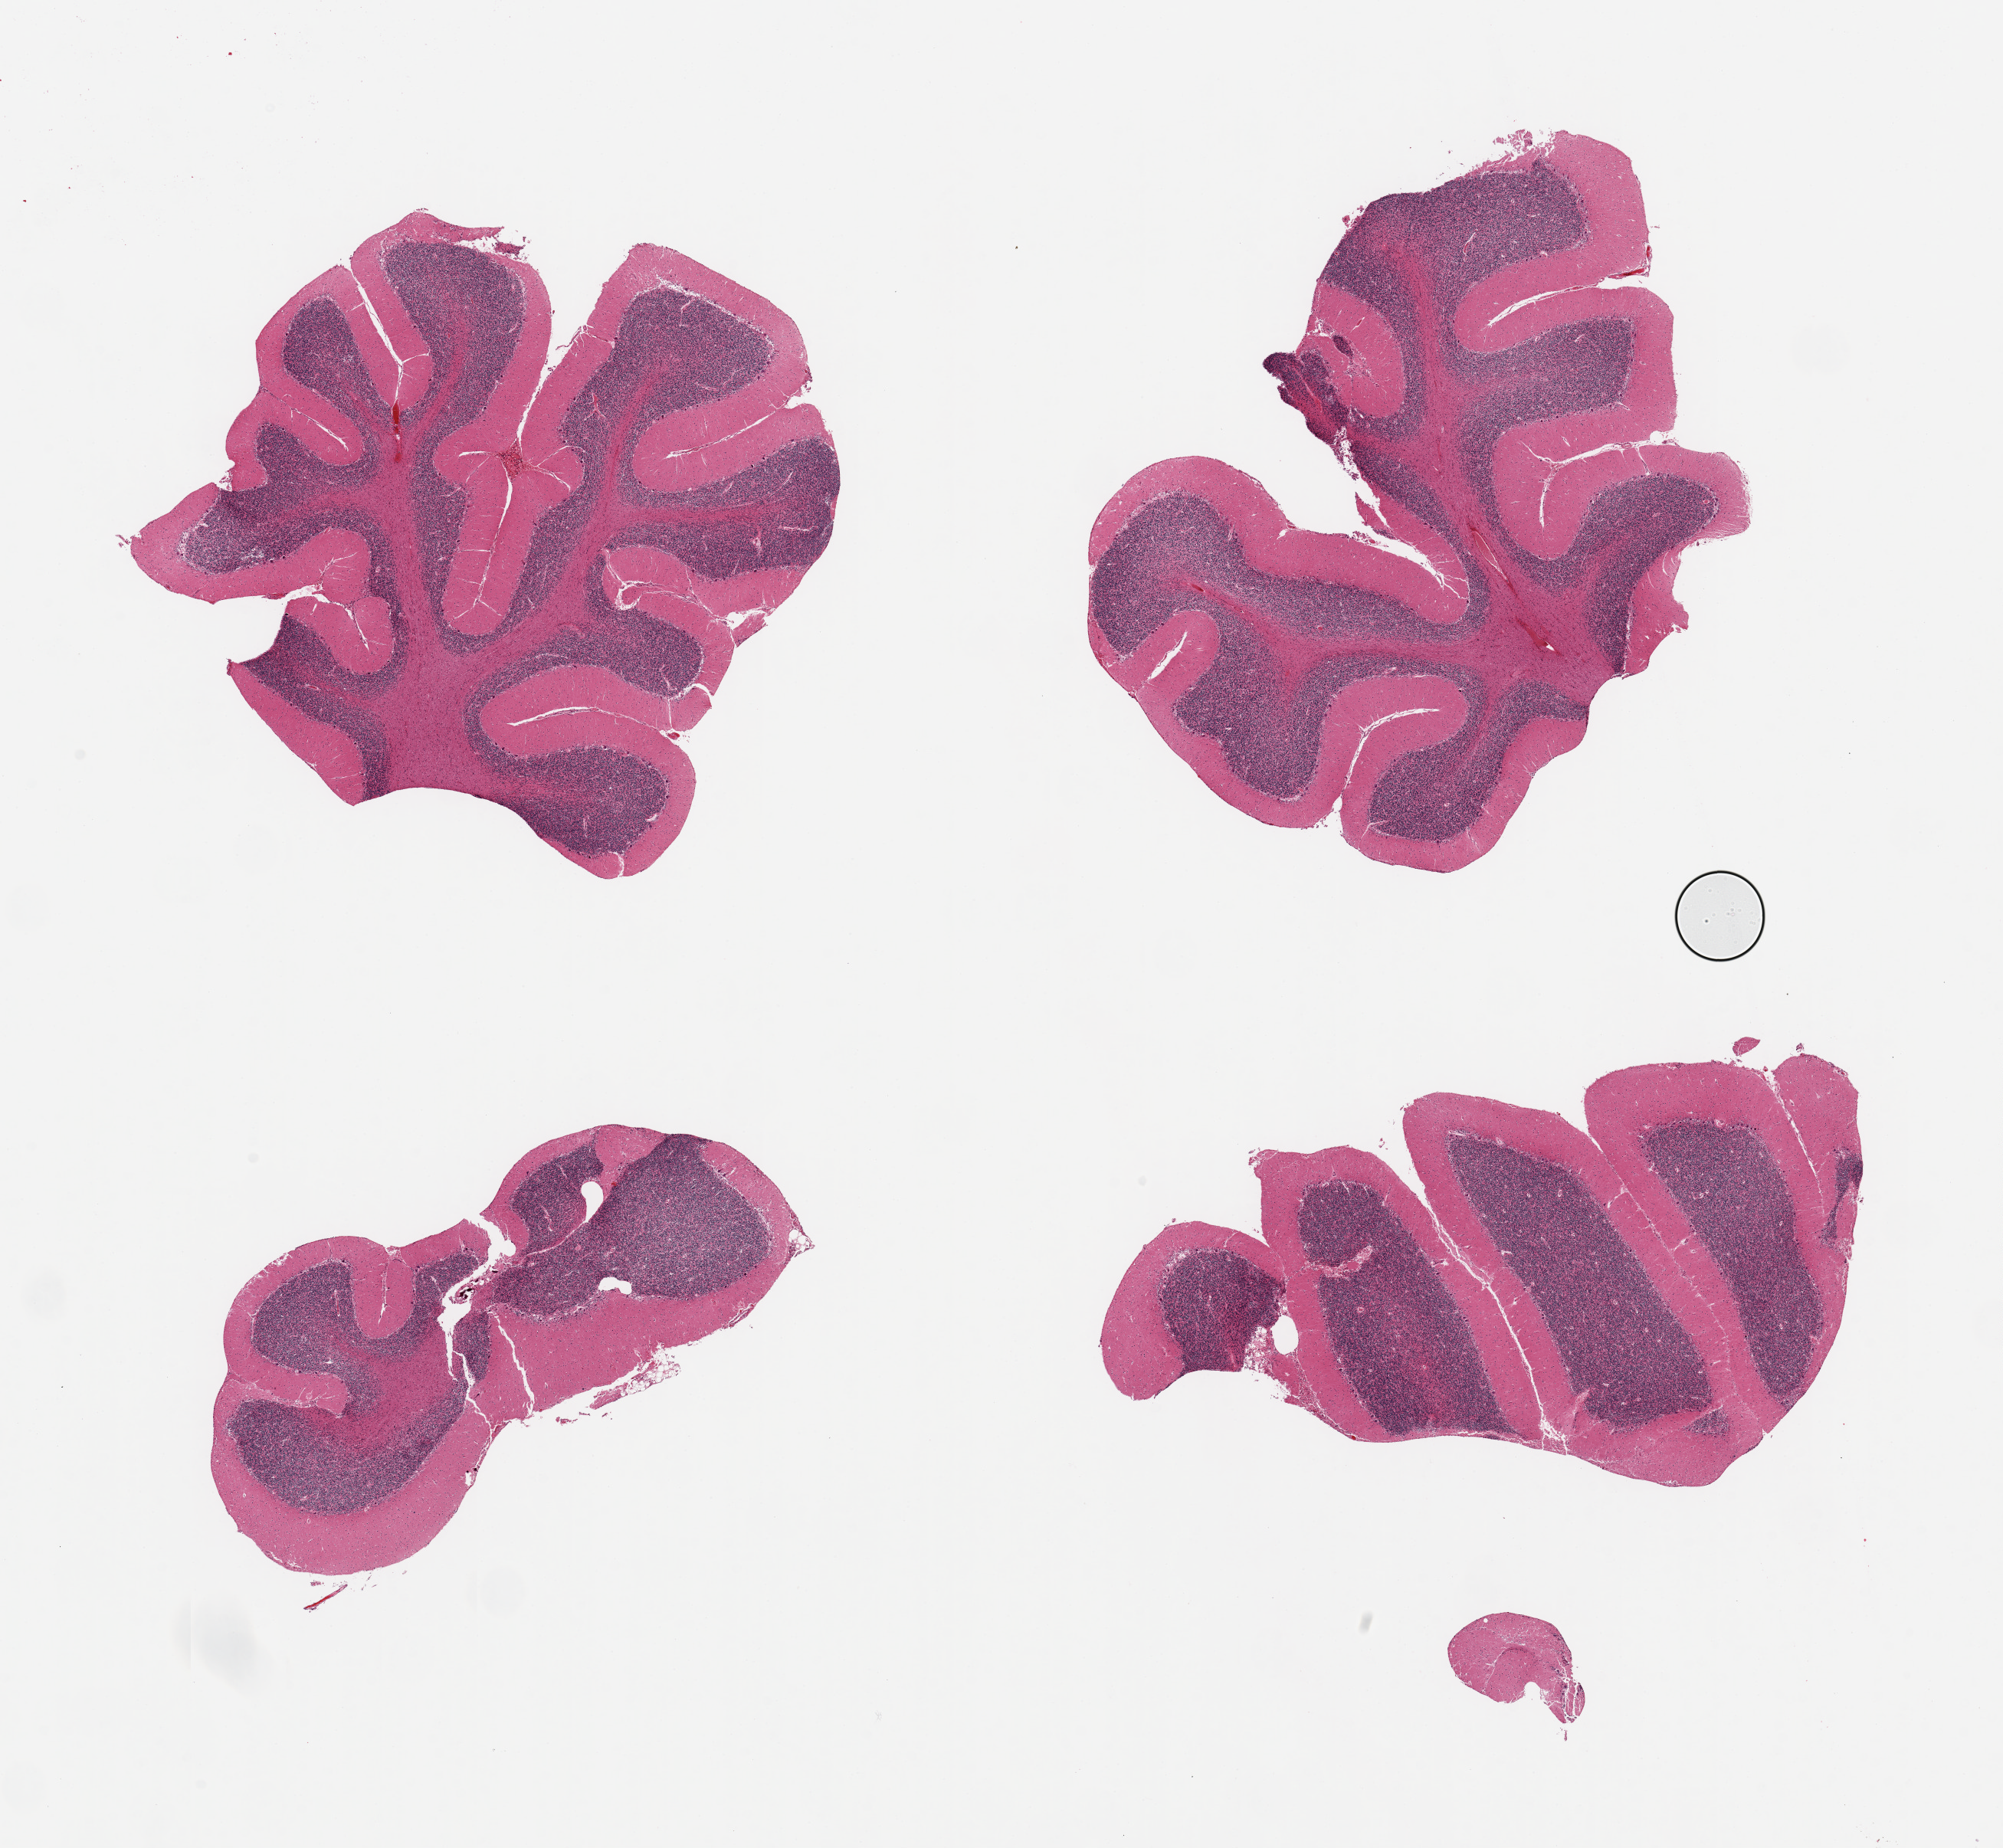
Digitized H&E-stained section — whole scanned area (about 20.7 x 19.1 mm, from a 20x scan) shown as a low-resolution overview, PAXgene-fixed paraffin-embedded (PFPE) section, target tissue: cerebellum, donor tissue sample. Donor sex: male.
• pathologist's review note for this sample: 4 pieces; some purkinje cells suggest hypoxic damage